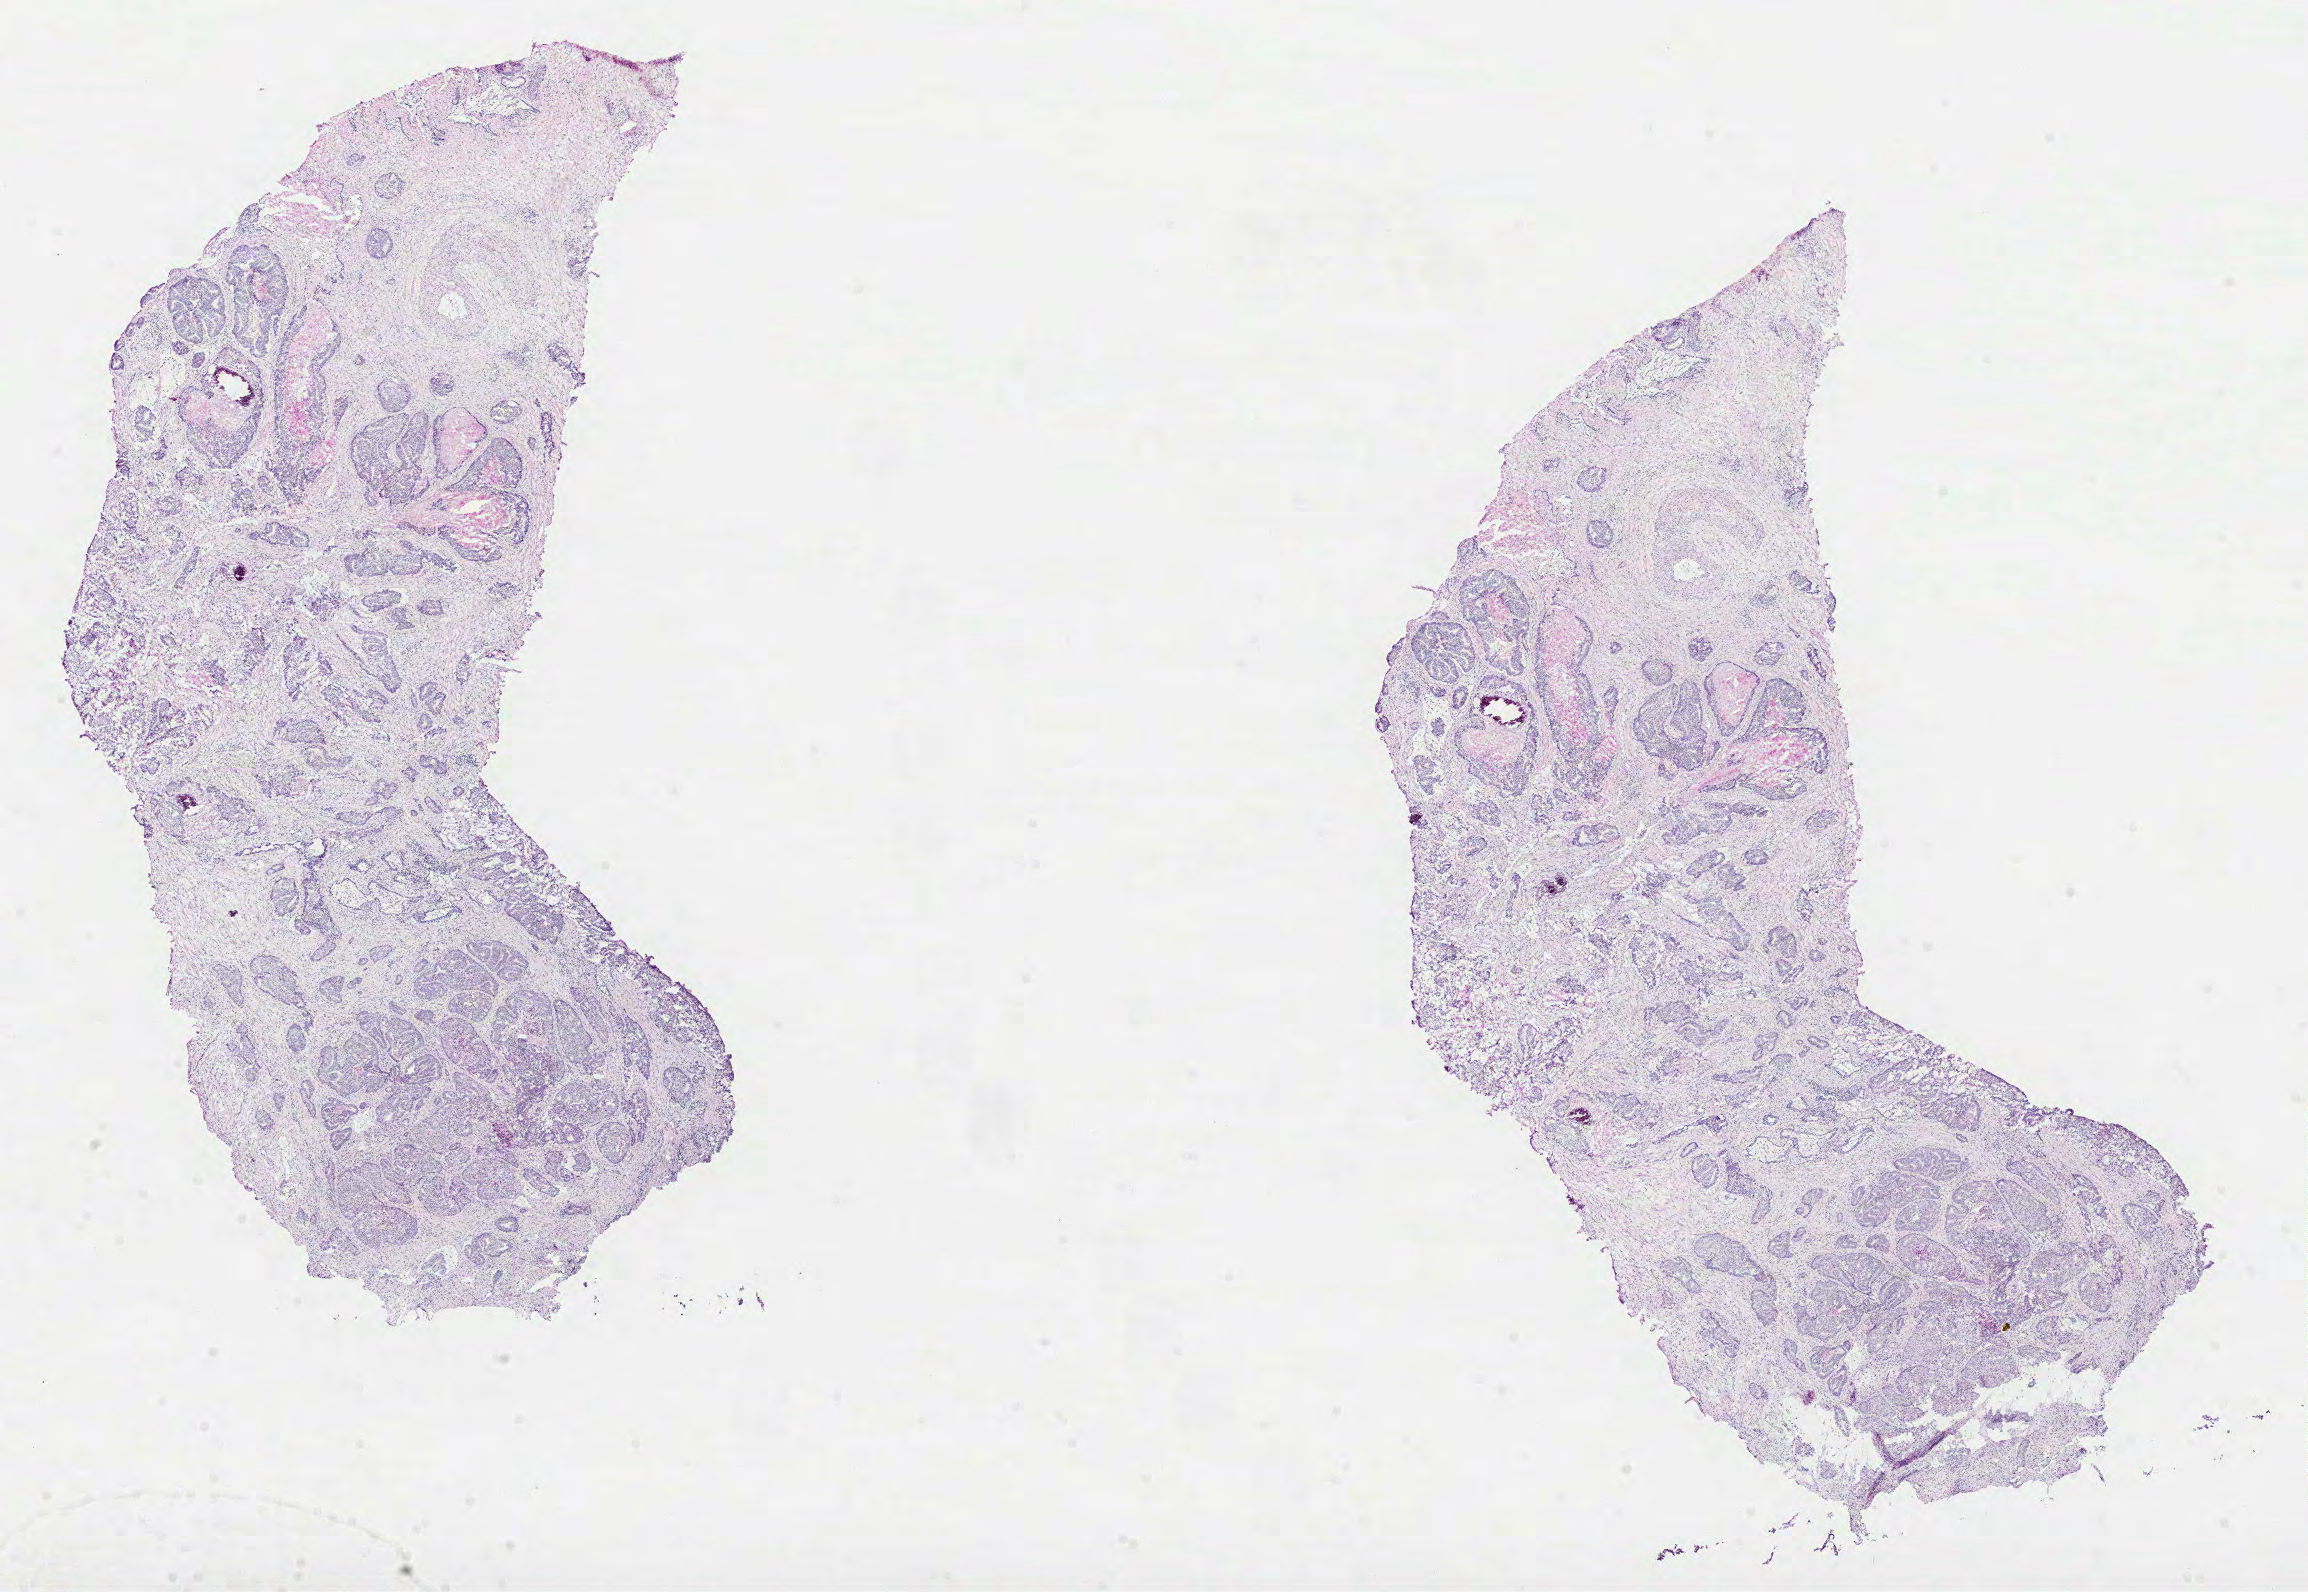
Hematoxylin and eosin (H&E) stained whole-slide image, a low-resolution overview of the entire scanned area, about 18.6 x 12.8 mm, formalin-fixed paraffin-embedded (FFPE) diagnostic section, primary tumour sample from the prostate. Patient: male, age at initial diagnosis 60 years. Gleason score: 7 (4+3).
- laterality: bilateral
- histologic diagnosis: Acinar cell carcinoma (prostate gland)
- lymph nodes positive (case pathology): 0 of 7 examined